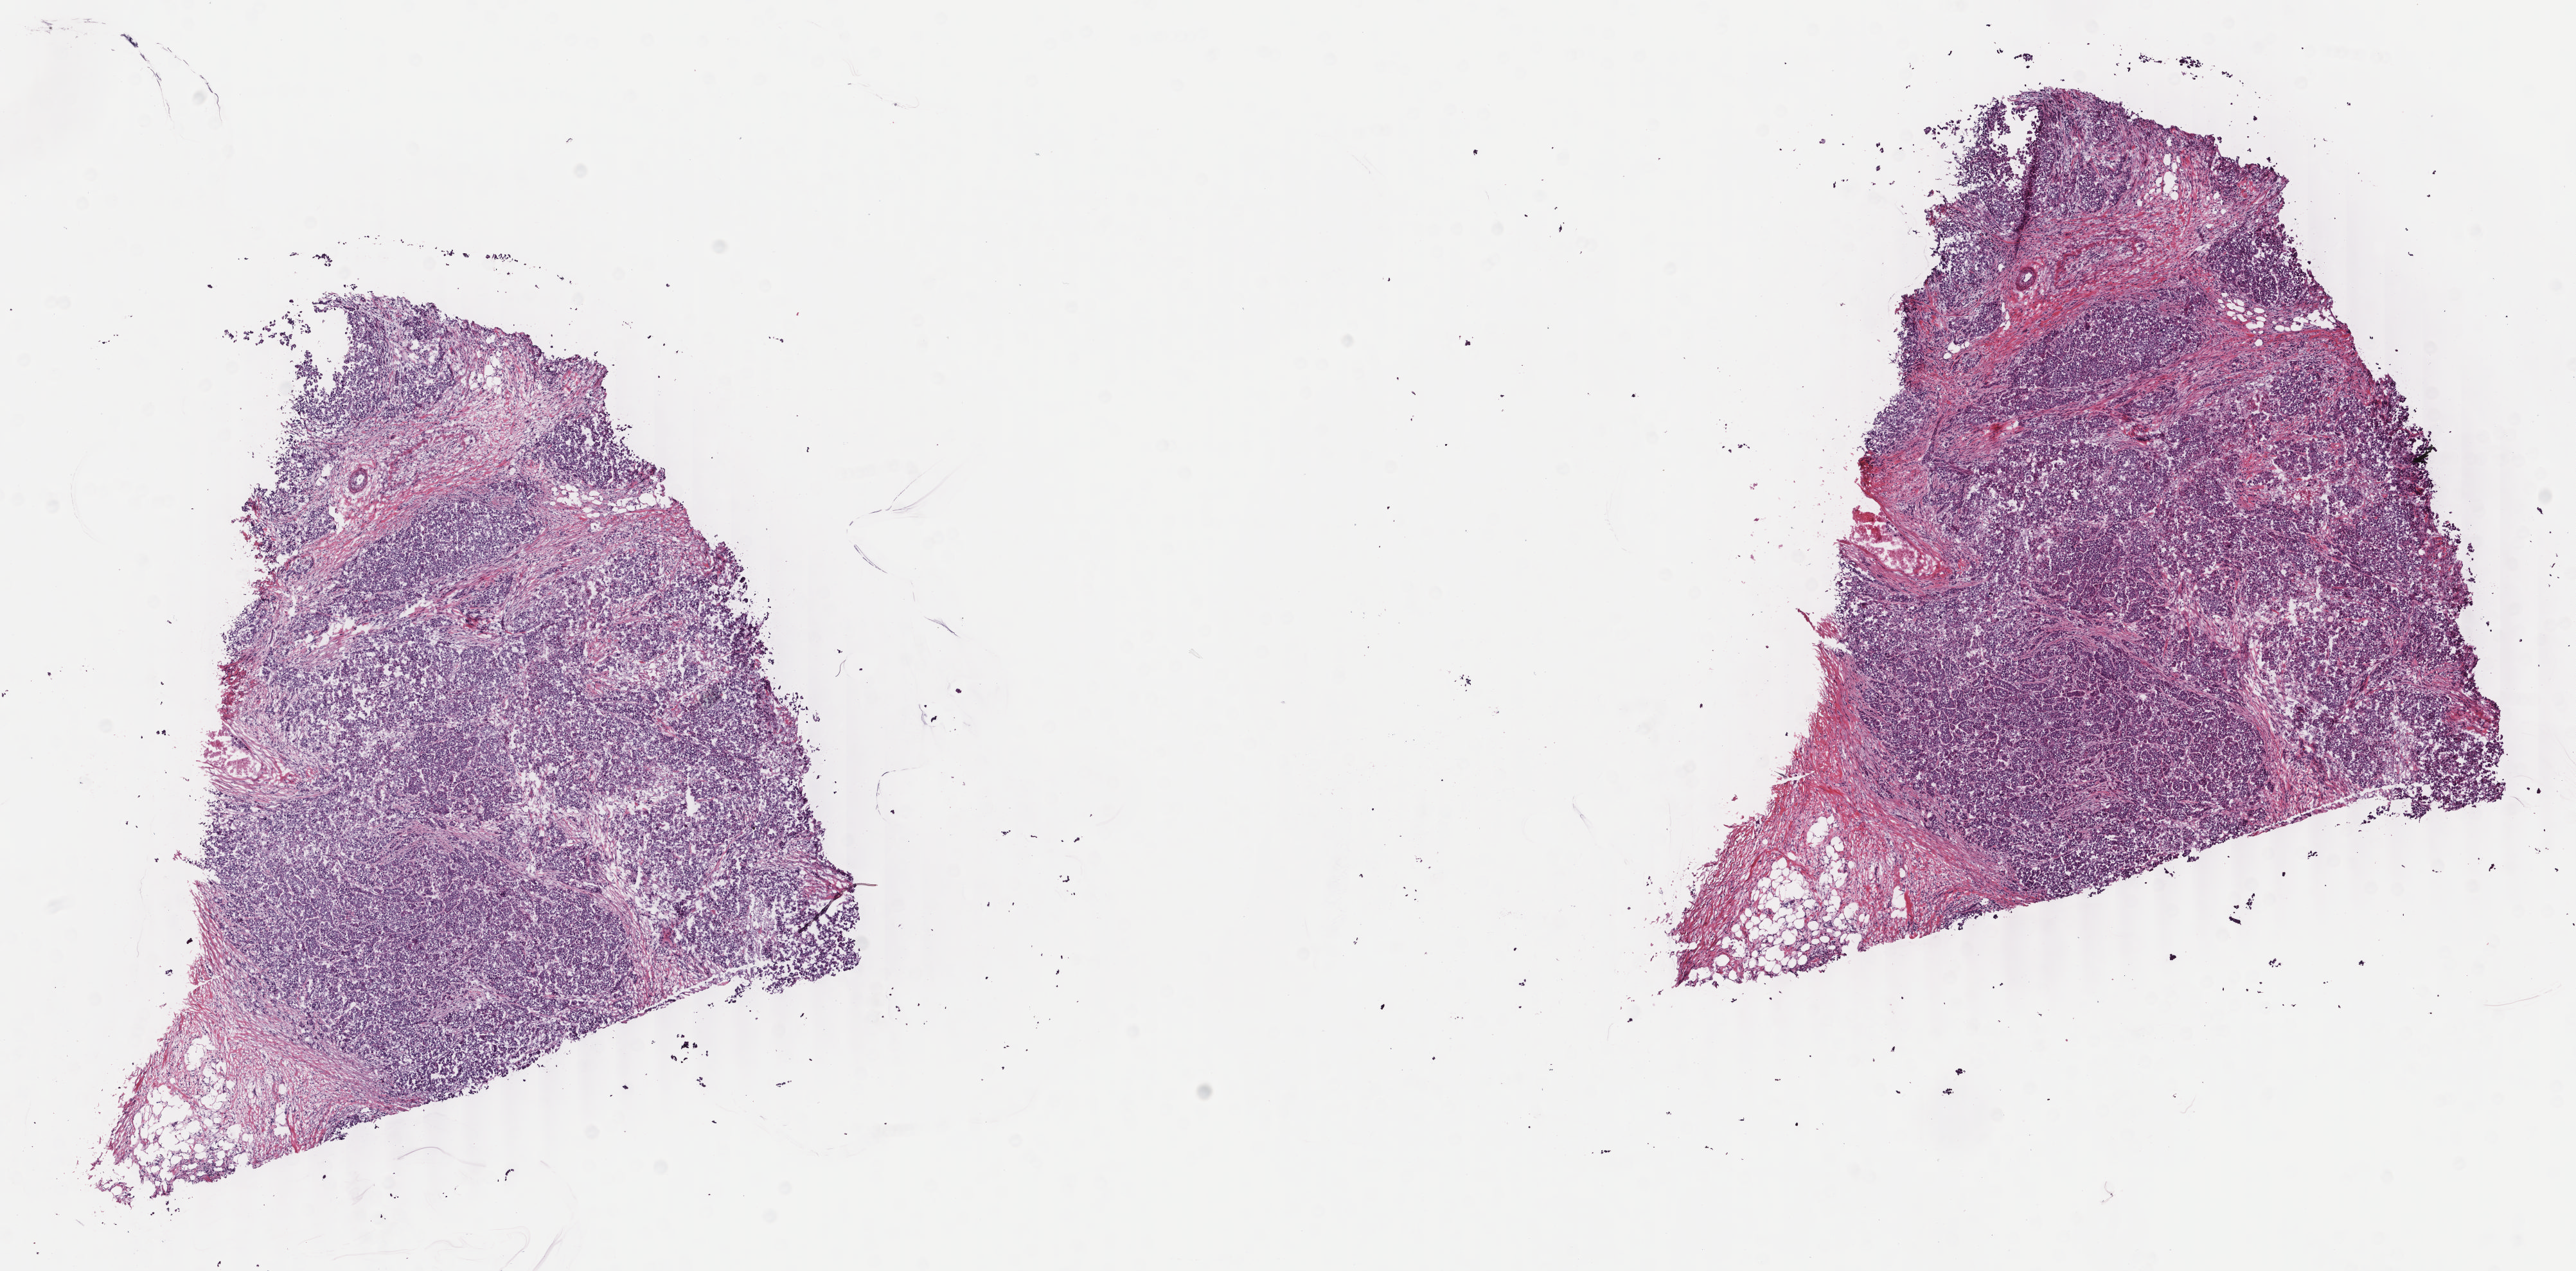
Whole-slide histology image, Hematoxylin and eosin (H&E) stained, whole scanned area (about 15.9 x 7.9 mm) shown as a low-resolution overview, frozen section, sample: primary tumour, breast. Female, age 53 years at initial diagnosis. Composition of this section per pathologist review: tumour cells 90%, tumour nuclei 80%, normal cells 0%, stromal cells 10%, necrosis 0%. Infiltration values recorded for this section: lymphocyte infiltration 0%, monocyte infiltration 0%, neutrophil infiltration 0%.
- lymph nodes positive (case pathology): 5 of 28 examined
- AJCC pathologic stage: IIIA
- histologic diagnosis: Infiltrating duct carcinoma, NOS